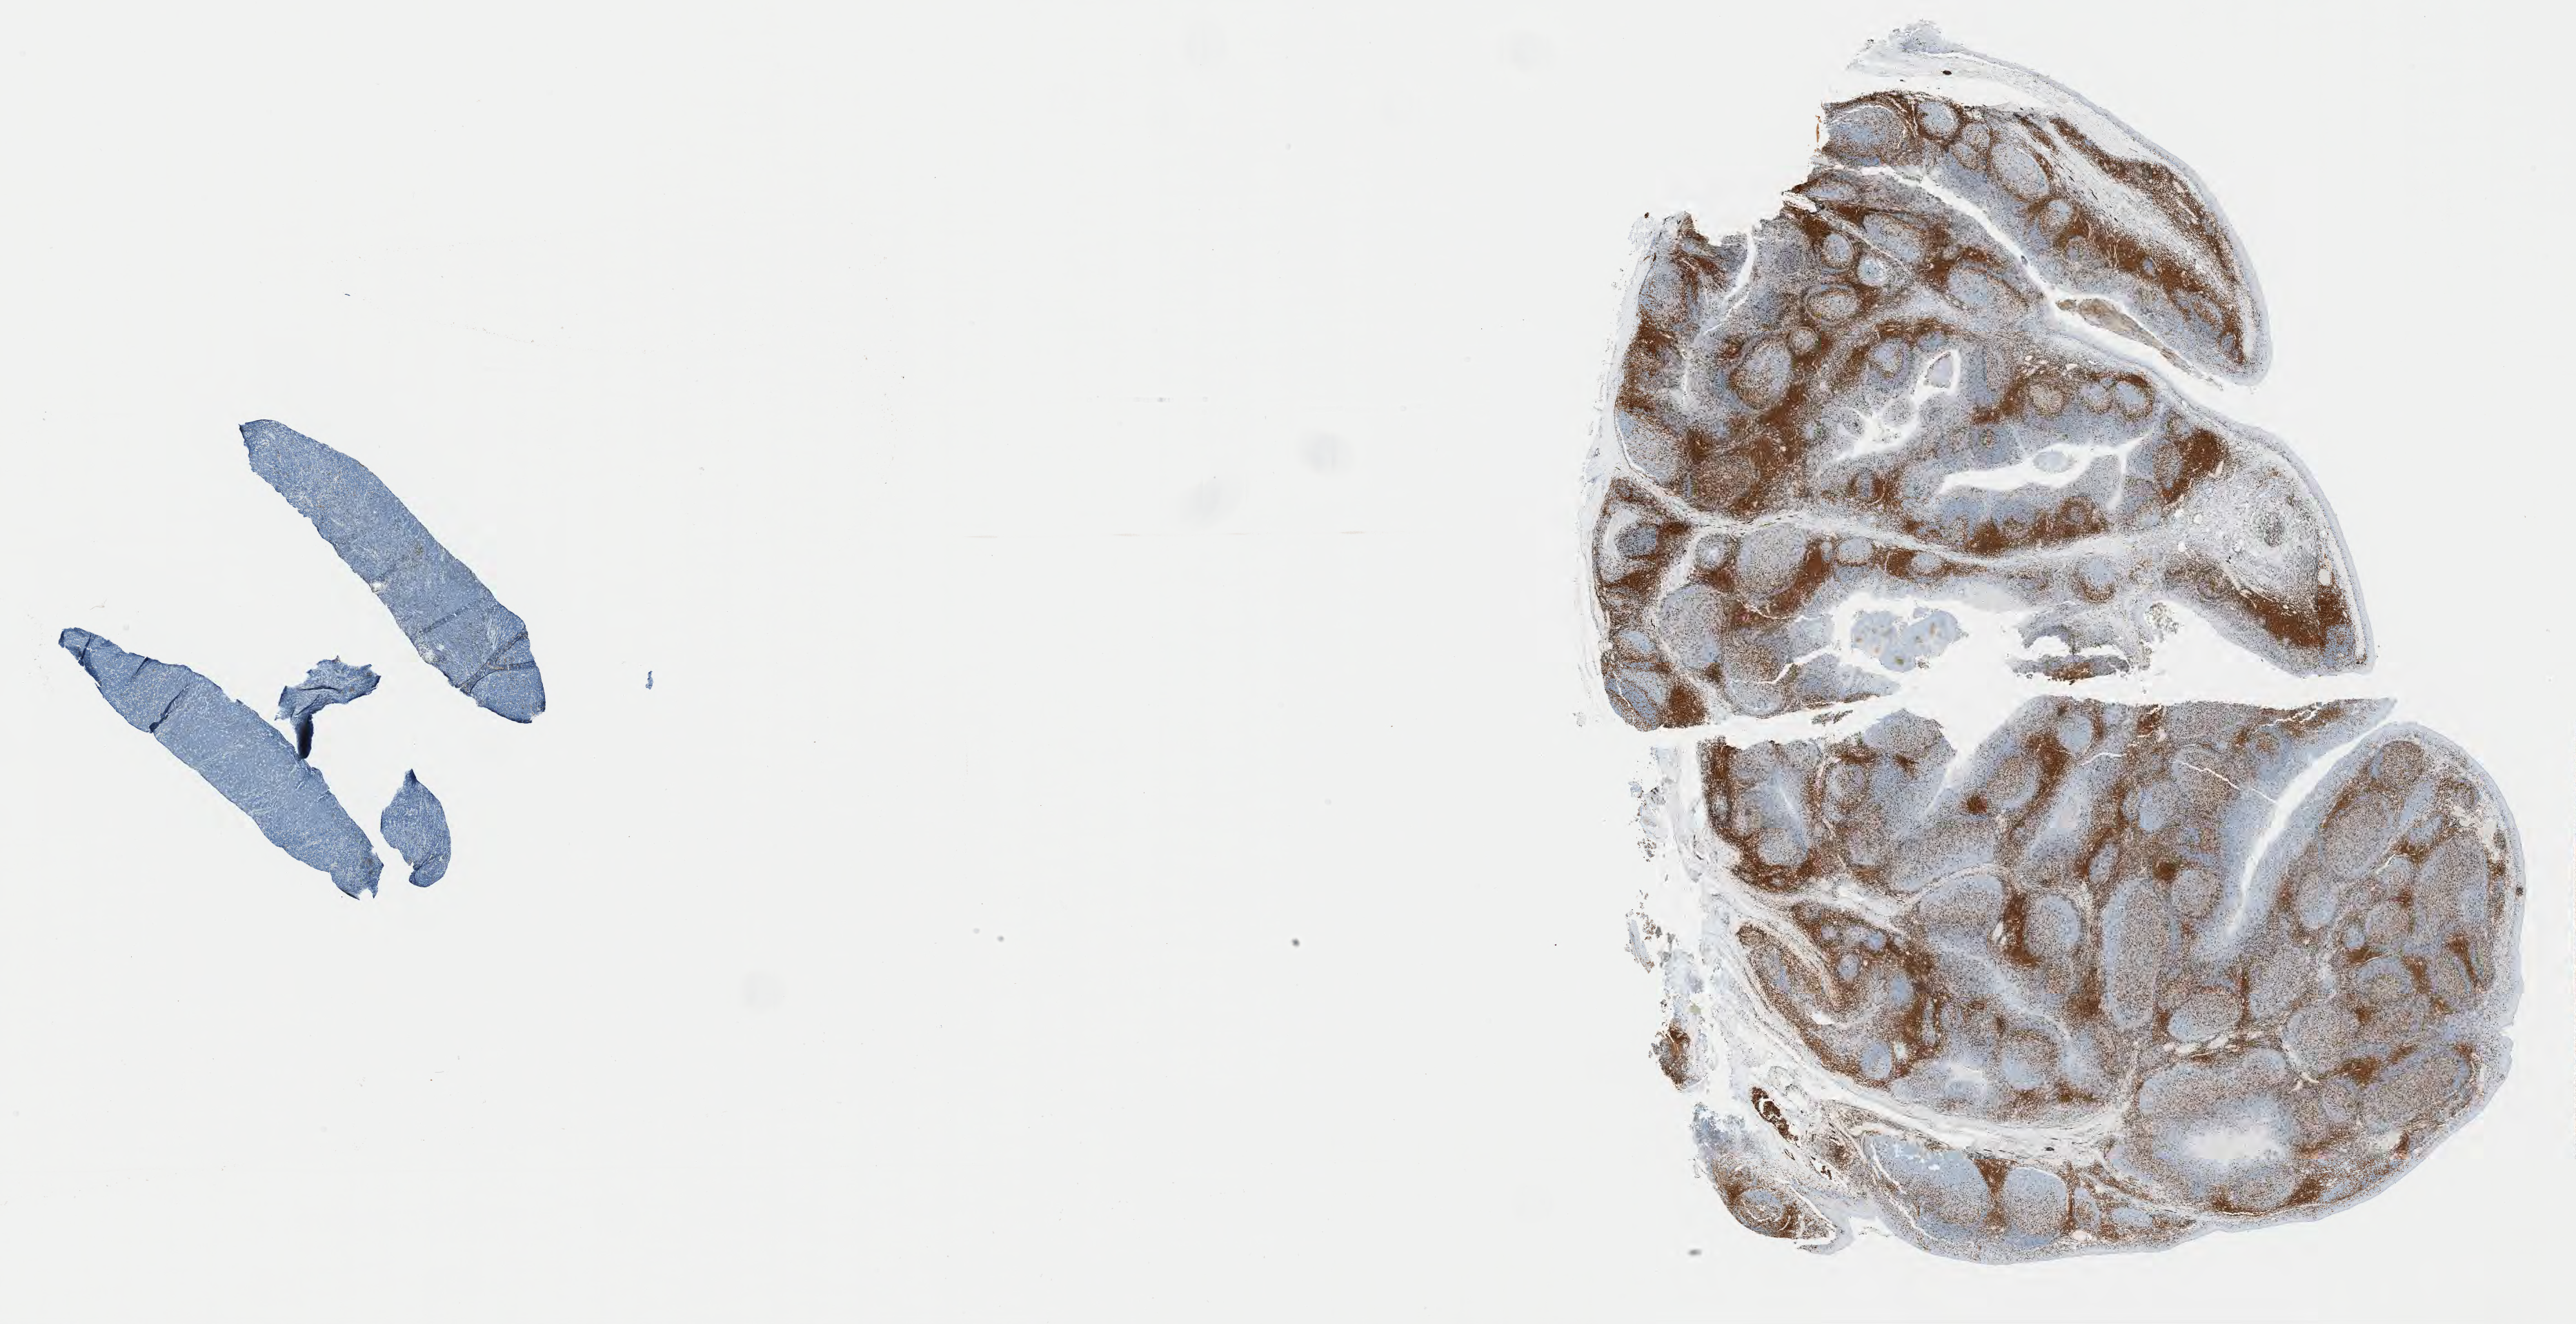
Whole-slide image, immunohistochemical stain for CD3 — whole scanned area (about 30.2 x 15.5 mm) shown as a low-resolution overview. Specimen: tumor tissue. Female patient, aged 46.
* diagnosis: Burkitt lymphoma, NOS